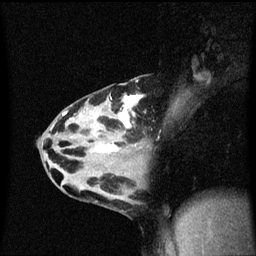
Breast MRI (dynamic contrast-enhanced), one sagittal slice; position 29 of 60 along the scan axis; dynamic contrast-enhanced series, image 2 of 3 at this slice position (ordered by acquisition); 1.5 T; TE 4.2 ms, TR 8.4 ms; 2 mm slice thickness; 256 × 256 image matrix. Patient: female, 32 years.
Structures marked on this image (semi-automatically segmented with operator editing):
- analysis volume of interest (the breast-tissue region the enhancement analysis was run in; not a lesion): bounding box <55,78,180,167> (left, top, right, bottom; pixels)
- tumour enhancement mask (voxels above the 70 % enhancement threshold inside the analysis volume of interest): <63,94,145,153>